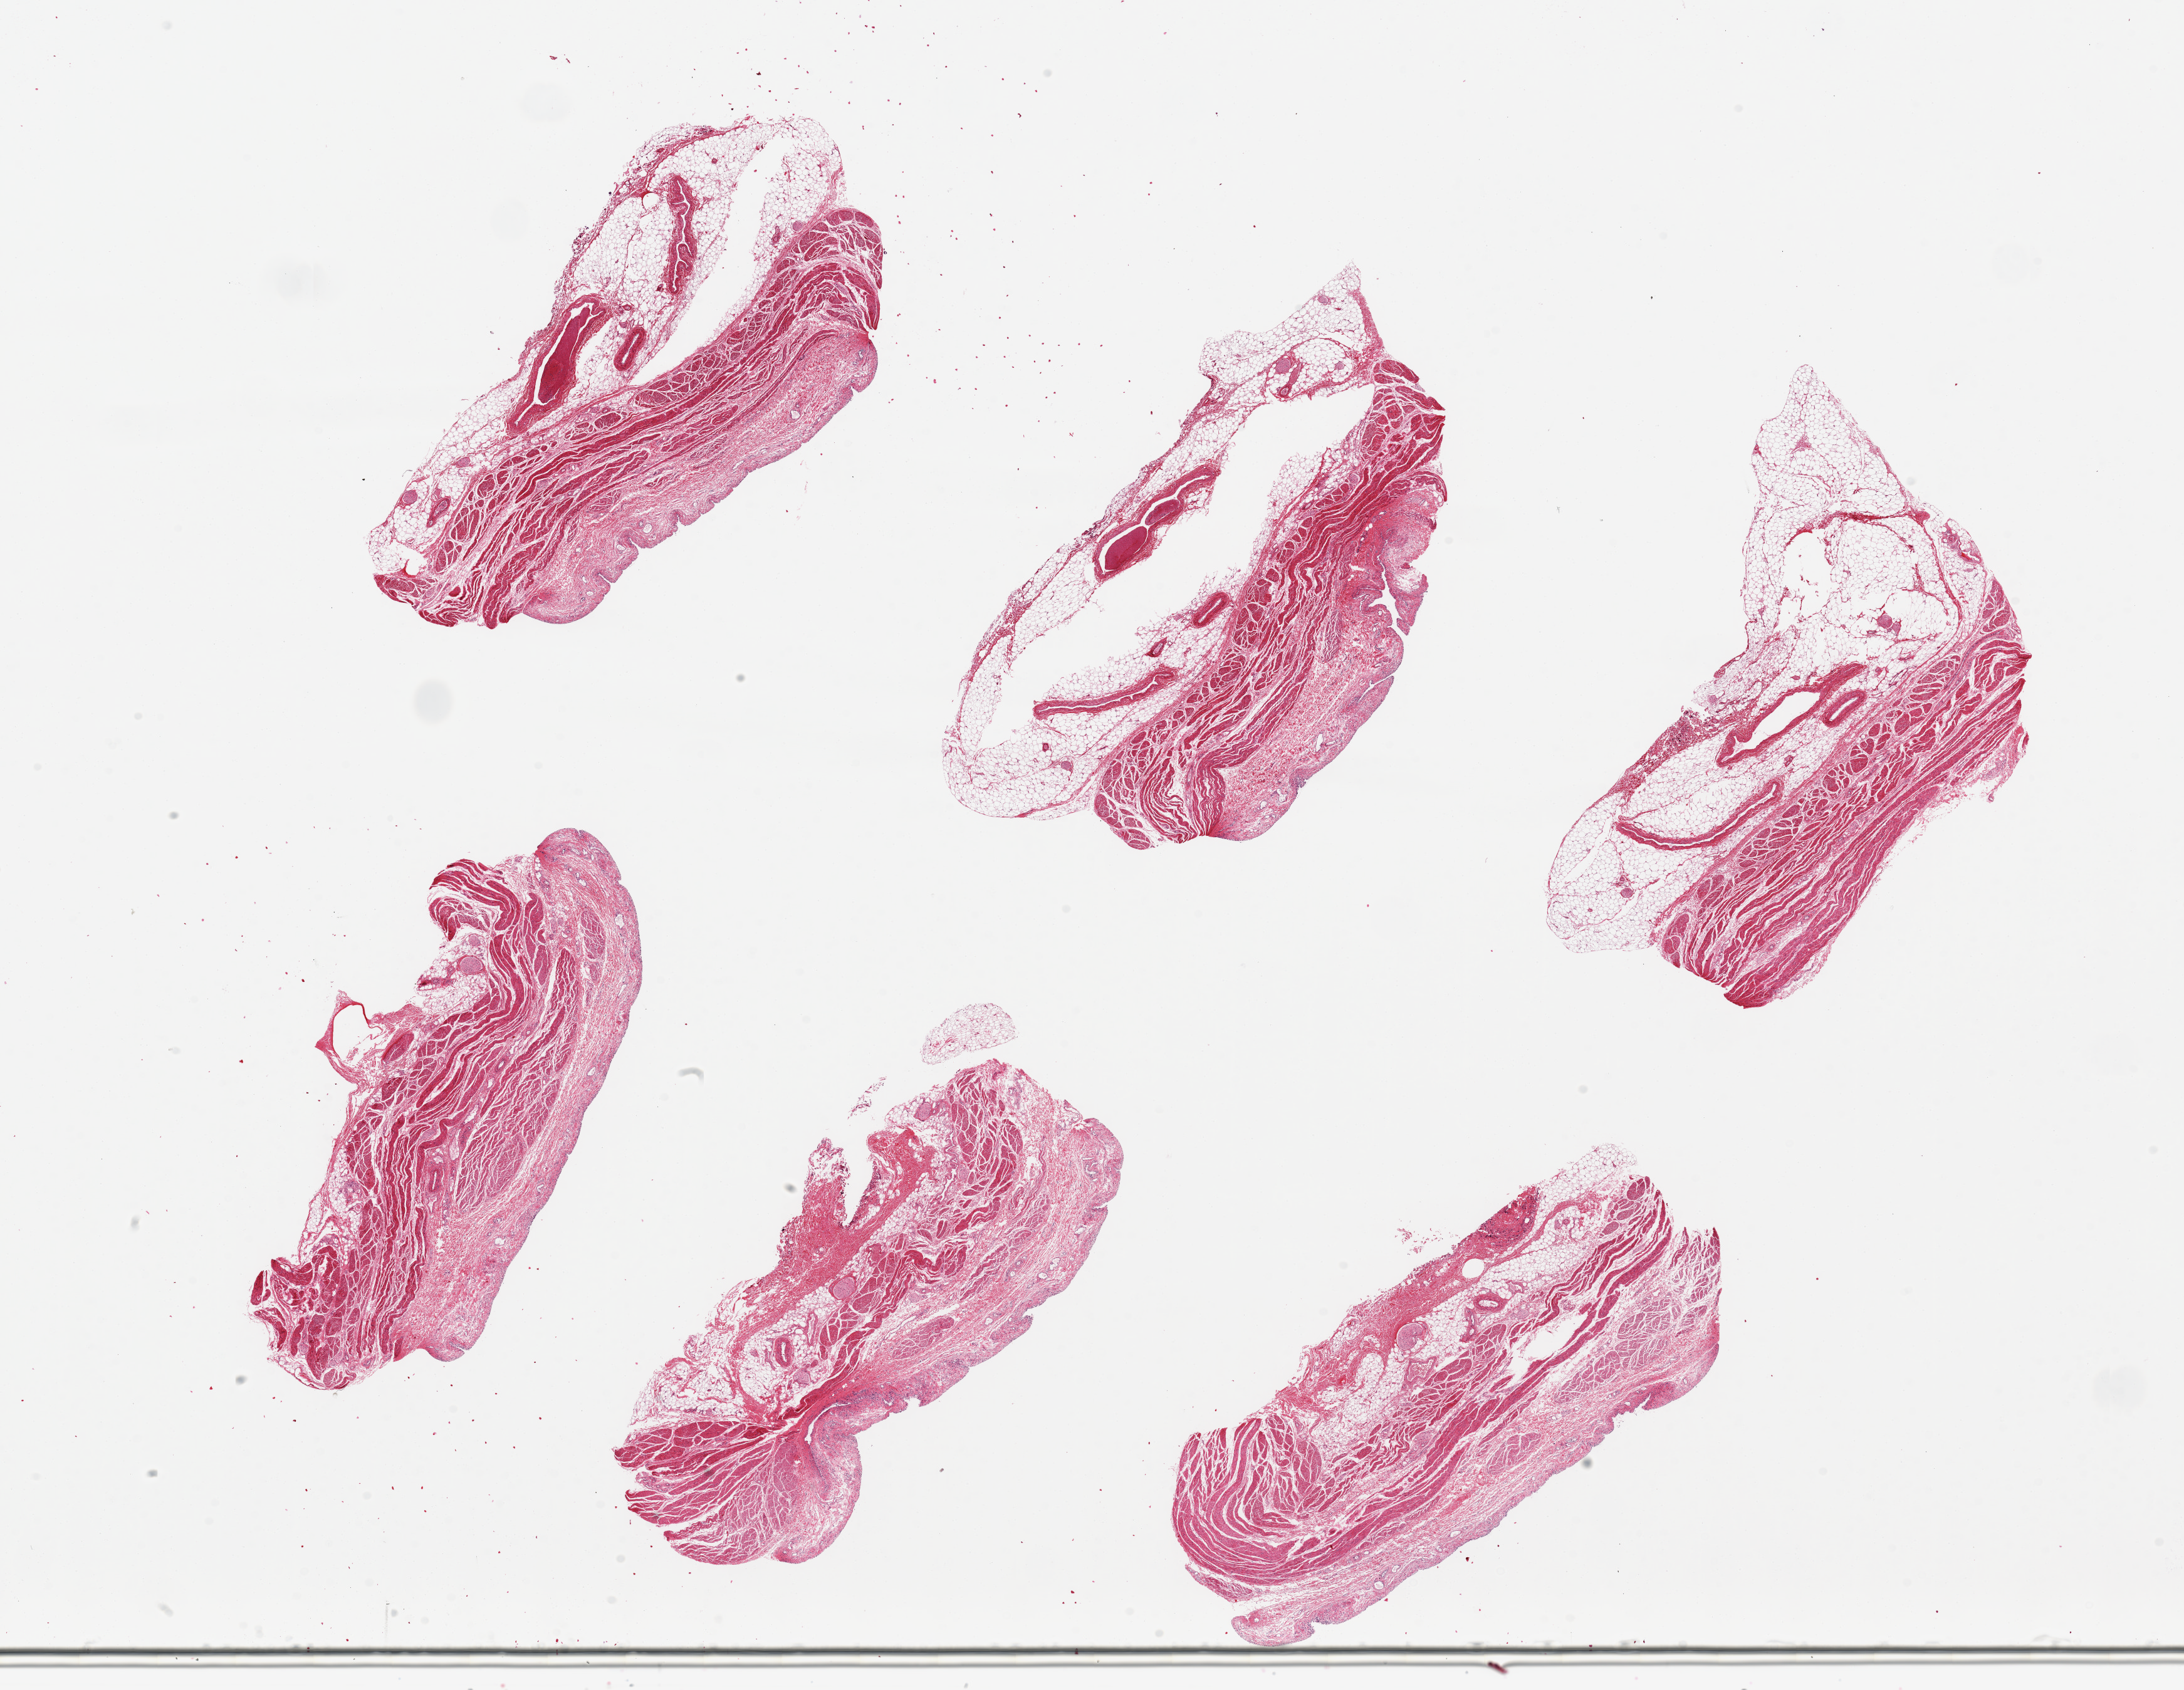
H&E whole-slide image — a low-resolution overview of the entire scanned area, about 27.6 x 21.3 mm (slide scanned at 20x), PAXgene-fixed, paraffin-embedded tissue, sampled site (target tissue): urinary bladder, tissue donor sample. Donor sex: male.
Pathologist's review note for this sample: 6 pieces up to 7x4 mm; epithelium totally sloughed; muscle preserved; abundant adipose (up to 3 mm thick) on deep side.